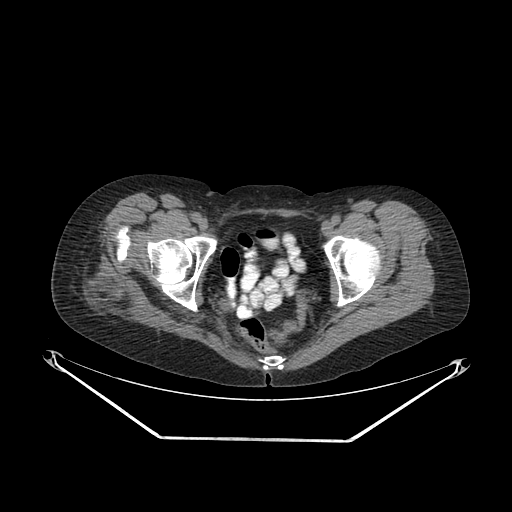
CT of an extremity soft-tissue mass (from a PET/CT study), one axial slice. Position 51 of 267 along the scan axis. Soft-tissue window (W 400 / L 40 HU). 3.75 mm slice thickness. 512 × 512 image matrix, field of view 500 × 500 mm. Female patient. From the clinical record (not read from this slice): histological type: epithelioid sarcoma with vascular differentiation; site of the primary tumour: right buttock.
Structures marked on this image (expert contour drawn on MRI and transferred to this co-registered scan by the dataset authors):
- gross tumour volume (mass): bounding box (x1, y1, x2, y2) in pixels: (73, 263, 147, 325)